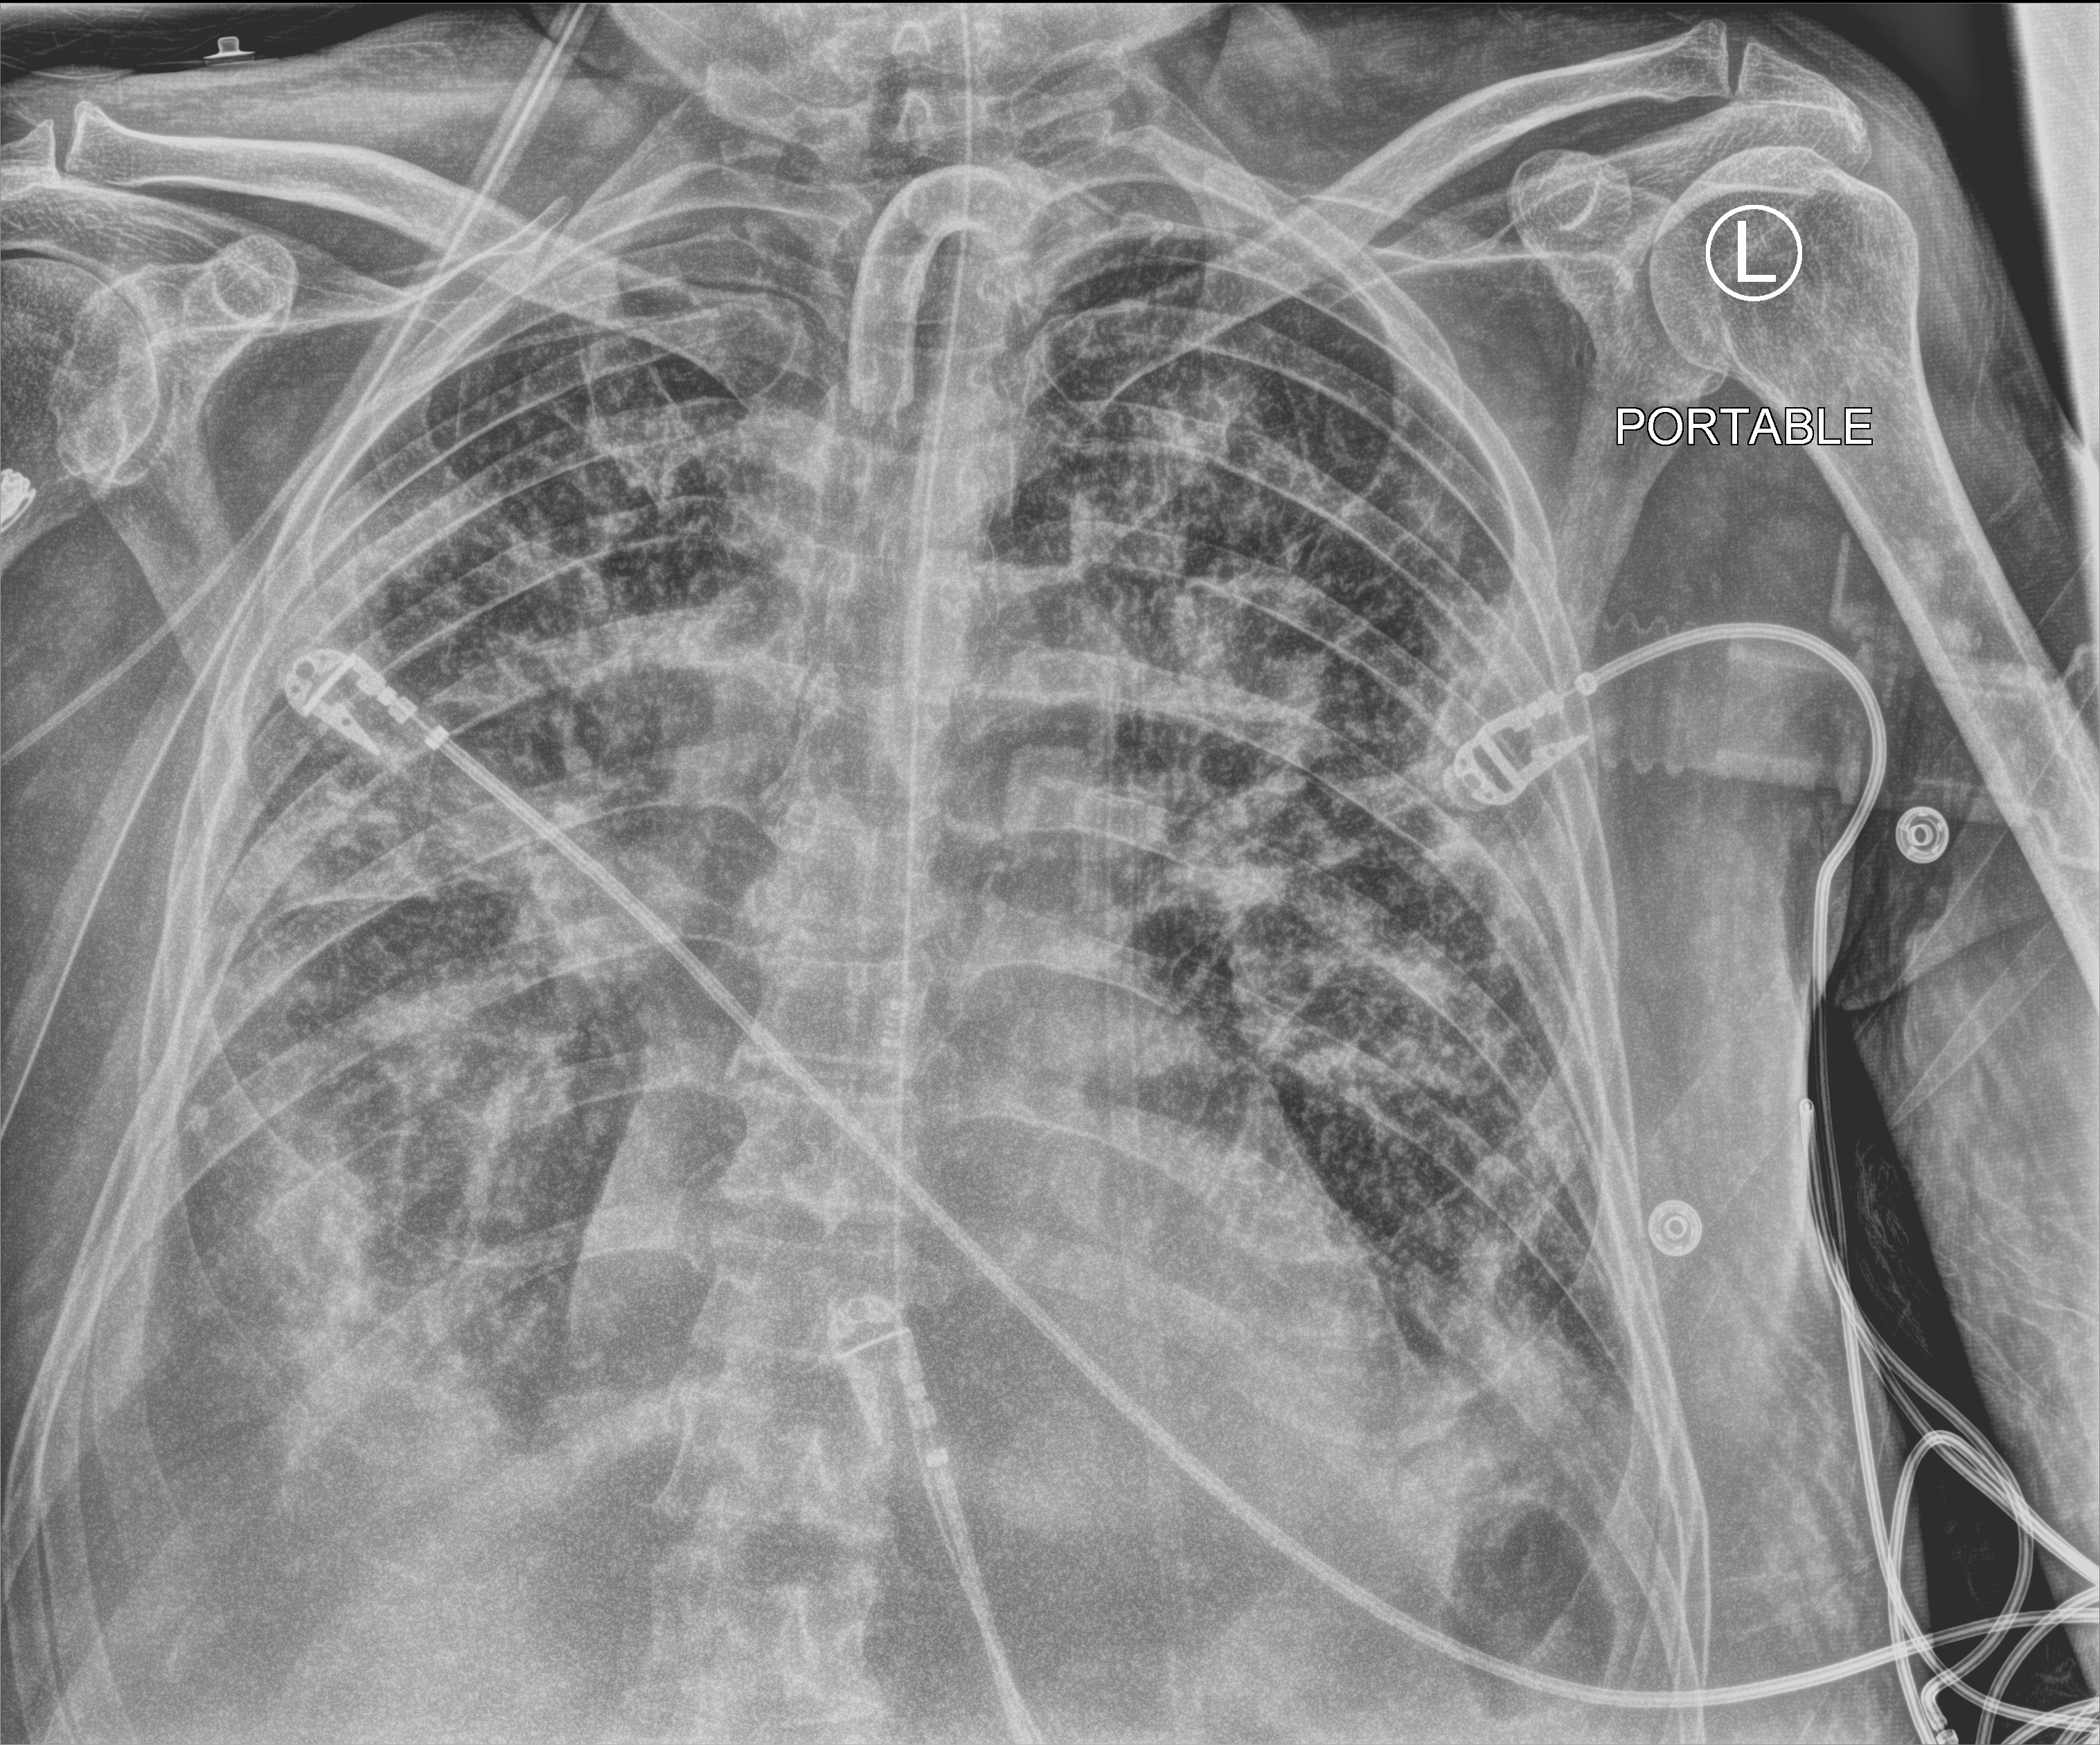
Chest X-ray (portable), anteroposterior (AP) projection. Patient hospitalised with COVID-19; male, aged 75–90 years.
From the hospital-stay record, not from the radiograph (when in the stay this image was taken is not recorded):
- mechanically ventilated during this hospital stay: yes